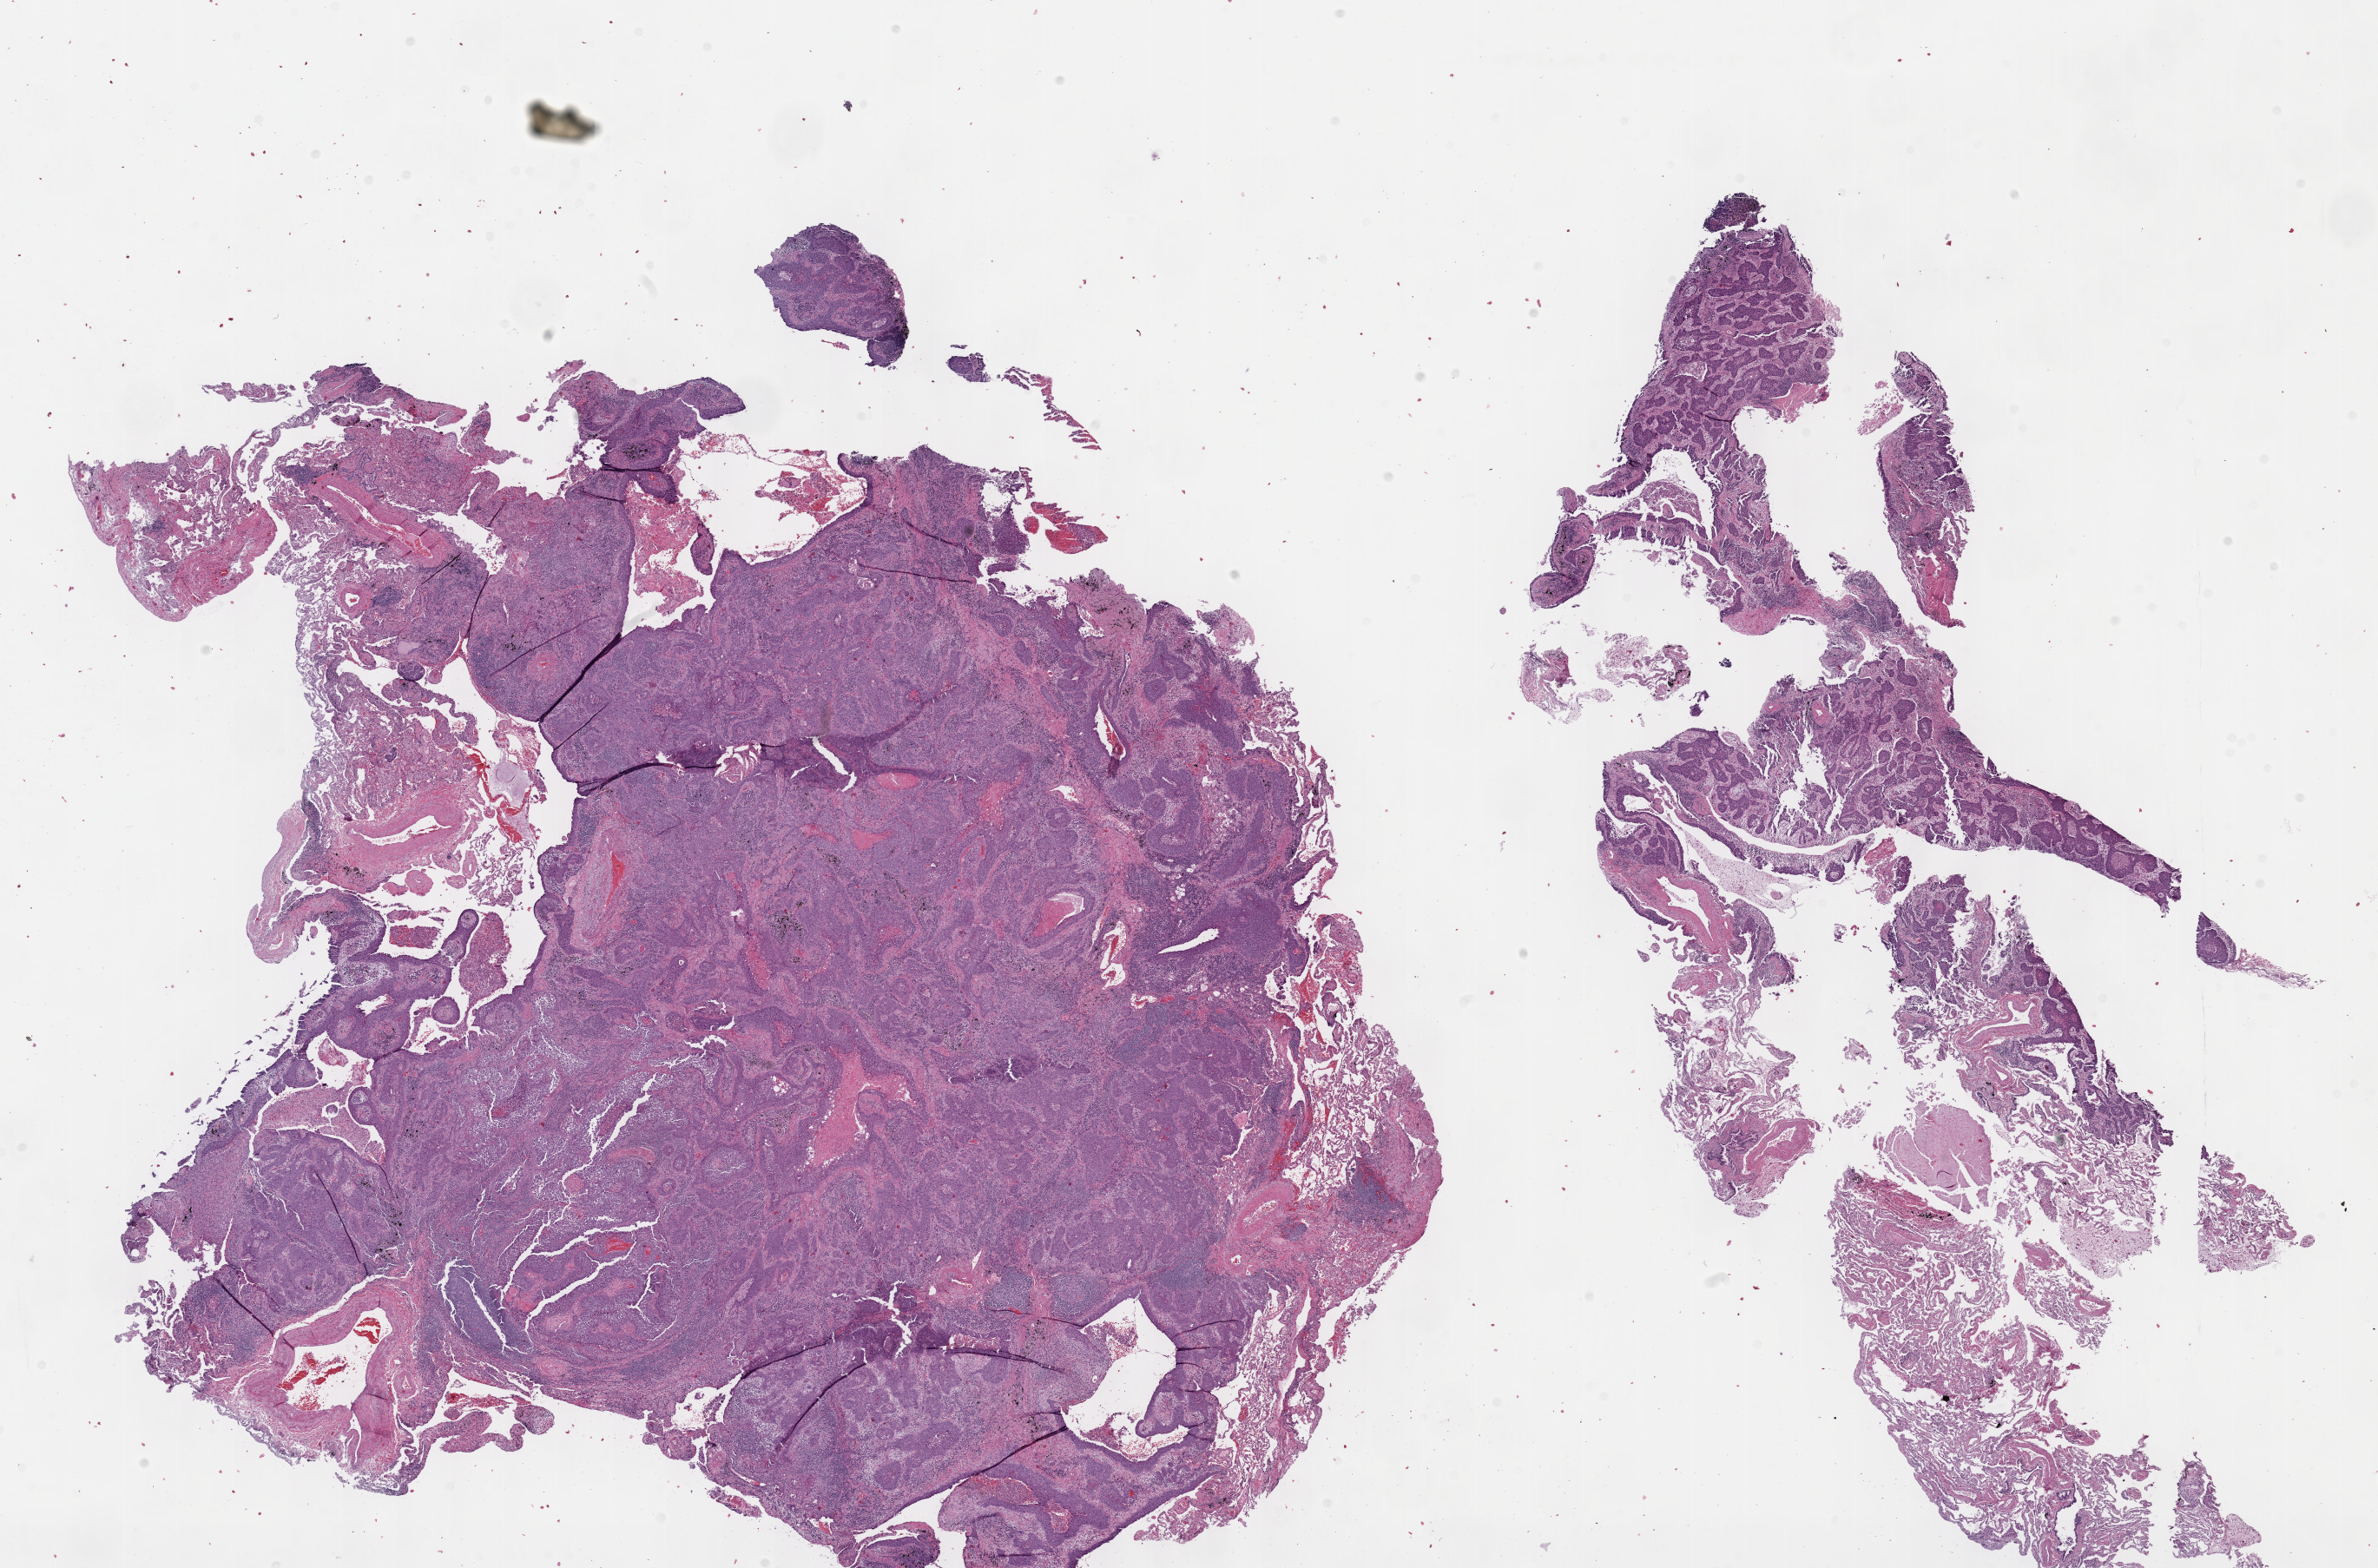
Digitized Hematoxylin and eosin (H&E) stained tissue section (whole slide) — a low-resolution overview of the entire scanned area, about 22.1 x 14.6 mm (acquisition: 40x scan); FFPE section; sample: primary tumour, lung. Female patient; age at initial diagnosis 73 years.
* pathologic diagnosis: Squamous cell carcinoma, NOS (upper lobe, lung)
* AJCC pathologic stage: IA